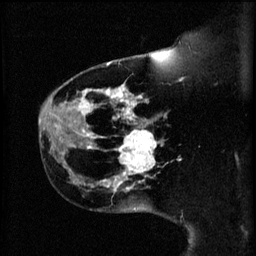
Breast MRI (dynamic contrast-enhanced), one sagittal slice. Position 44 of 60 along the scan axis. 3 images stored at this slice position (order not interpretable as contrast timing). 1.5 T. TE 4.2 ms, TR 11 ms. 256 × 256 image matrix, field of view 180 × 180 mm. Female patient, age 44 years.
Outlined on this slice (semi-automatically segmented with operator editing):
- analysis volume of interest (the breast-tissue region the enhancement analysis was run in; not a lesion): box from (x=114, y=124) to (x=165, y=179) px
- tumour enhancement mask (voxels above the 70 % enhancement threshold inside the analysis volume of interest): (x=114, y=124)–(x=157, y=179)